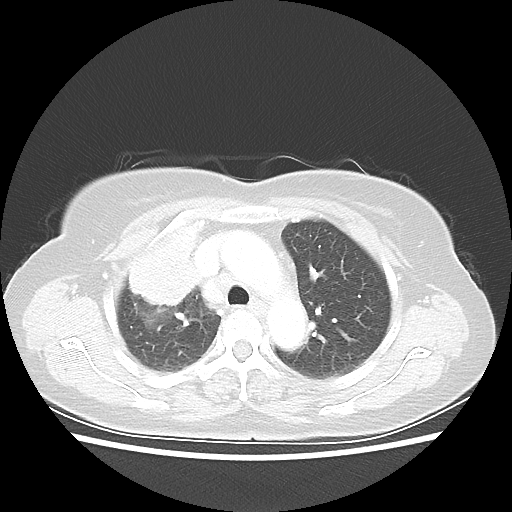
Chest CT, one axial slice; position 39 of 55 along the scan axis; reconstruction kernel LUNG; 80 kVp; lung window (W 1500 / L -600 HU); 5 mm slice thickness; 512 × 512 image matrix, field of view 337 × 337 mm. Female patient, age 62 years. Case-level facts recorded for this patient, not image findings: clinical TNM (as recorded): T4 N3 M0.
Annotated regions visible in this slice (rectangle marked by the reading radiologist):
- lung tumour (recorded histology: squamous cell carcinoma): bounding box (x1, y1, x2, y2) in pixels: (117, 204, 212, 306)